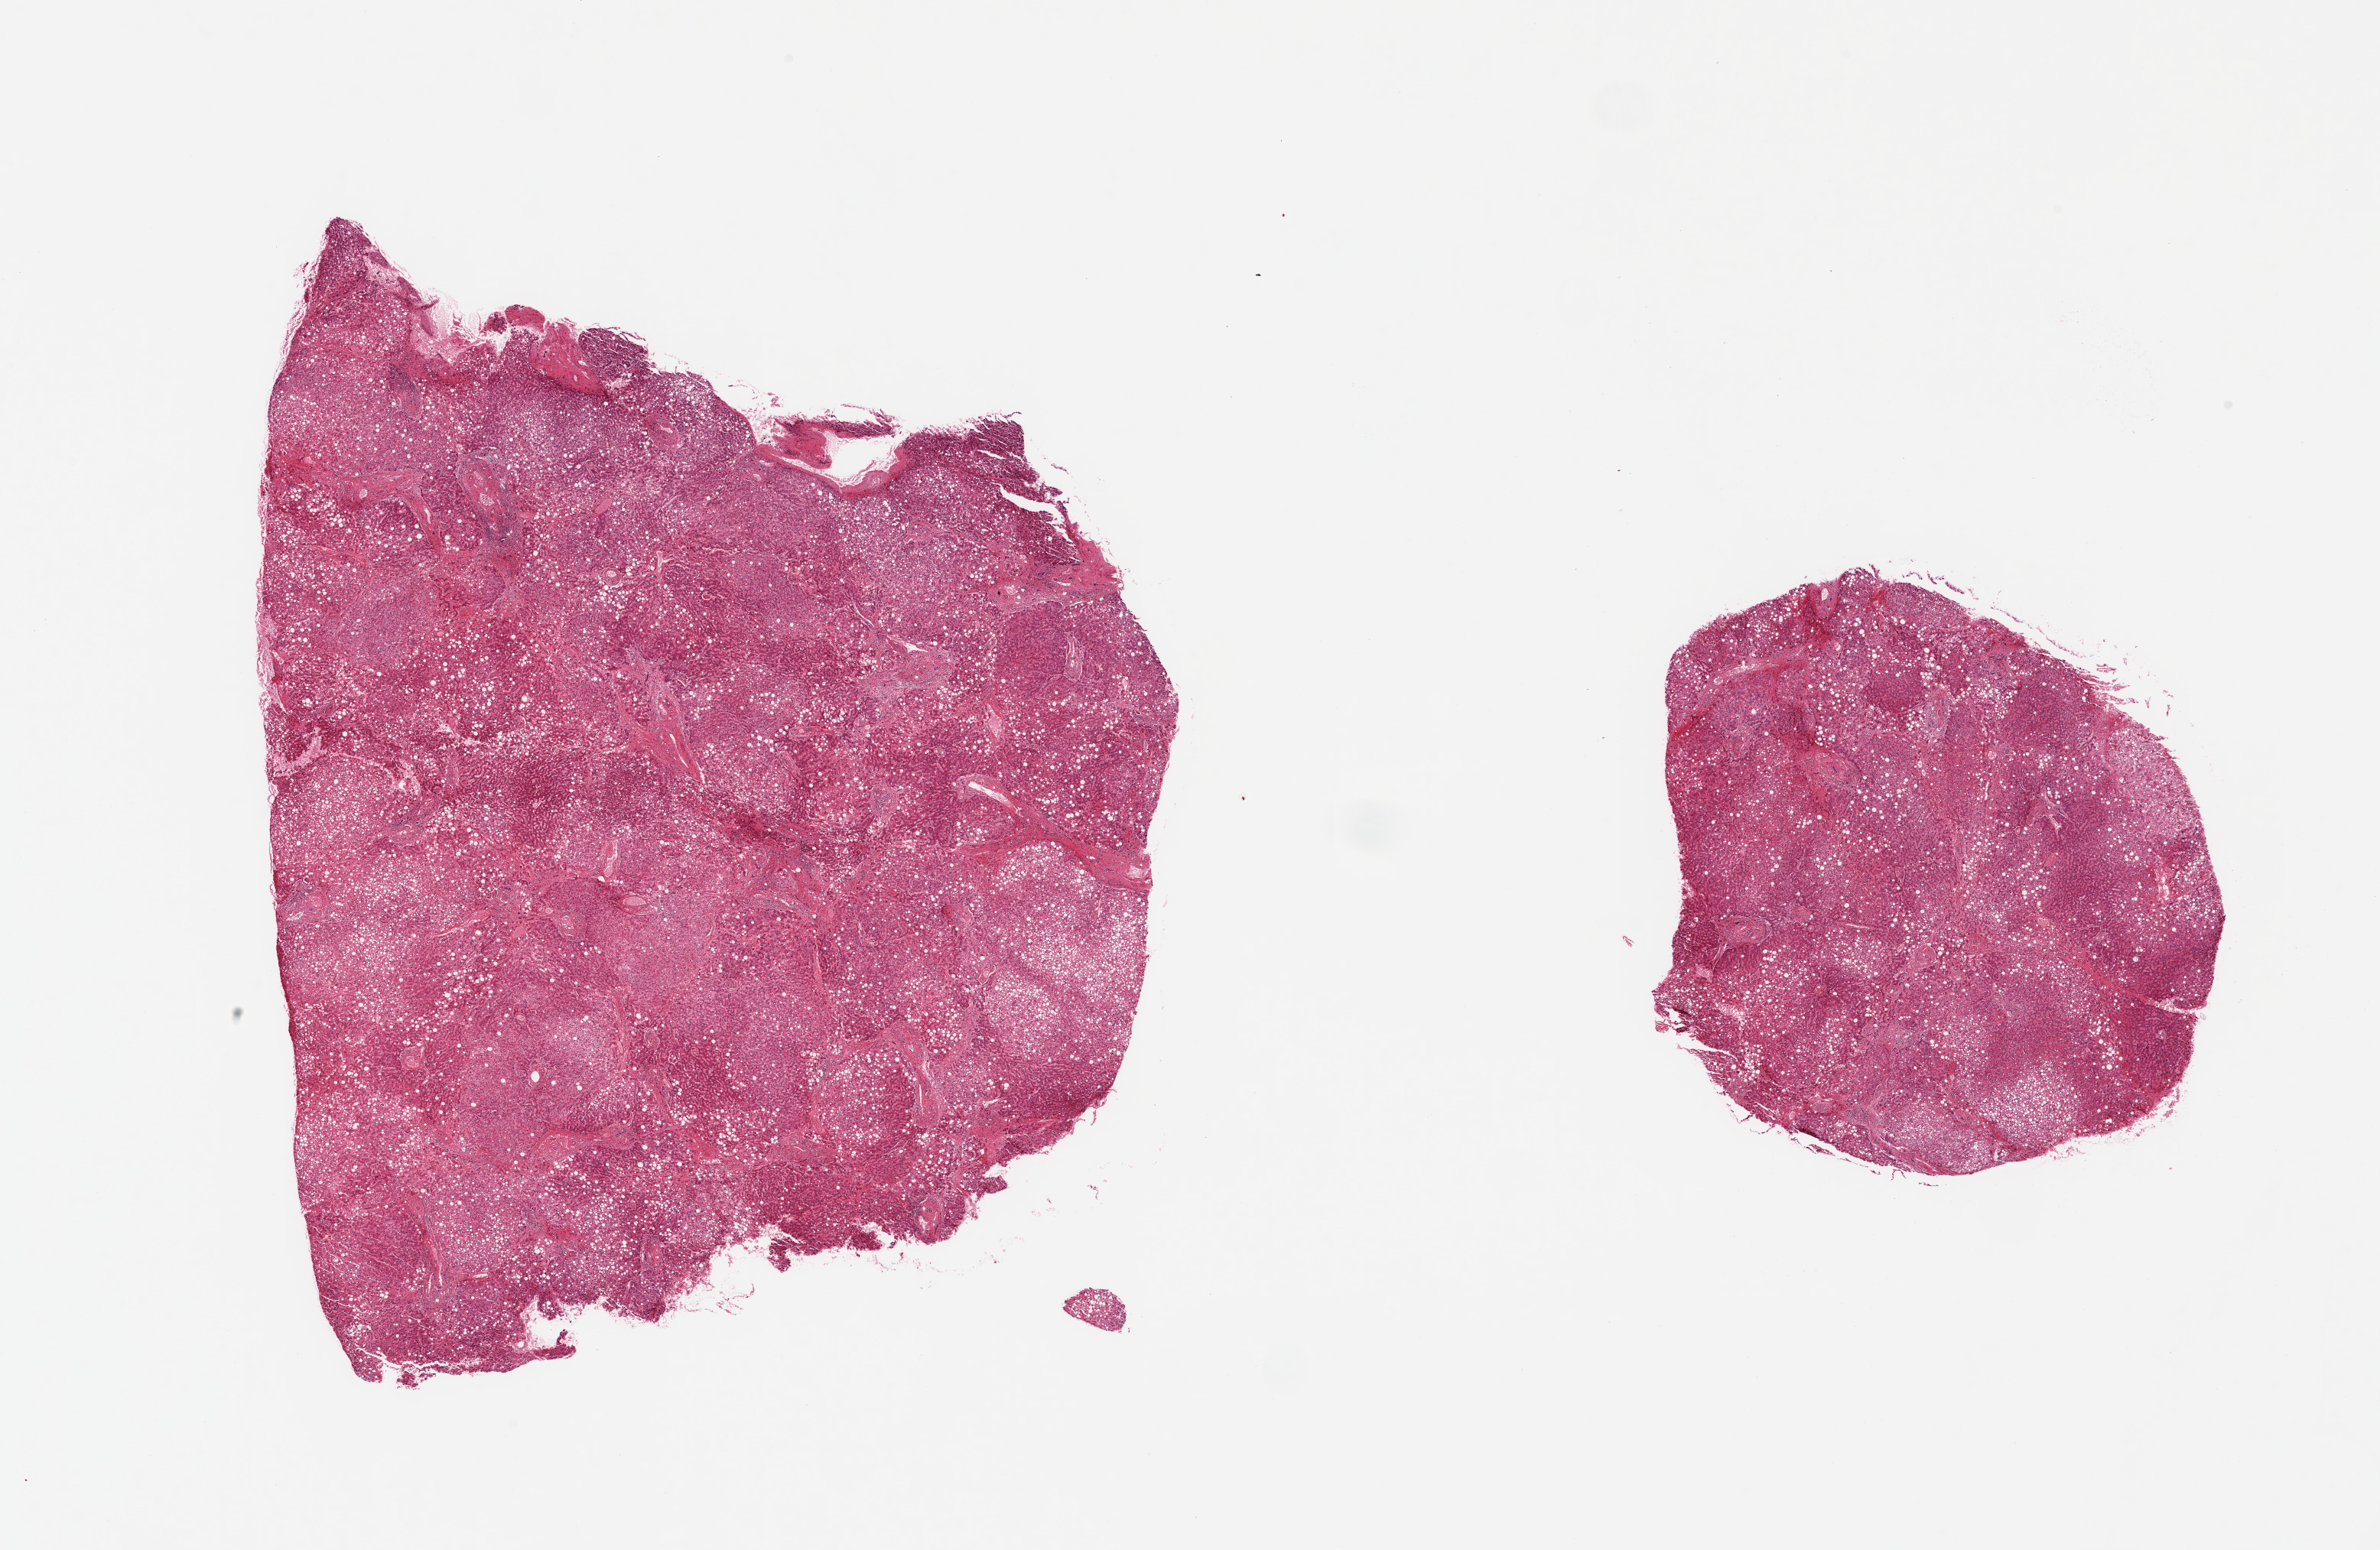
Haematoxylin and eosin whole-slide image — shown as a low-resolution overview of the whole scanned area (about 24.6 x 16.0 mm, slide scanned at 20x); PAXgene-fixed paraffin-embedded (PFPE) section; section of liver (target tissue); tissue donor sample. Female donor.
* review note (as recorded): 2 pieces; moderate to severe centrilobular macrovesicular steatosis